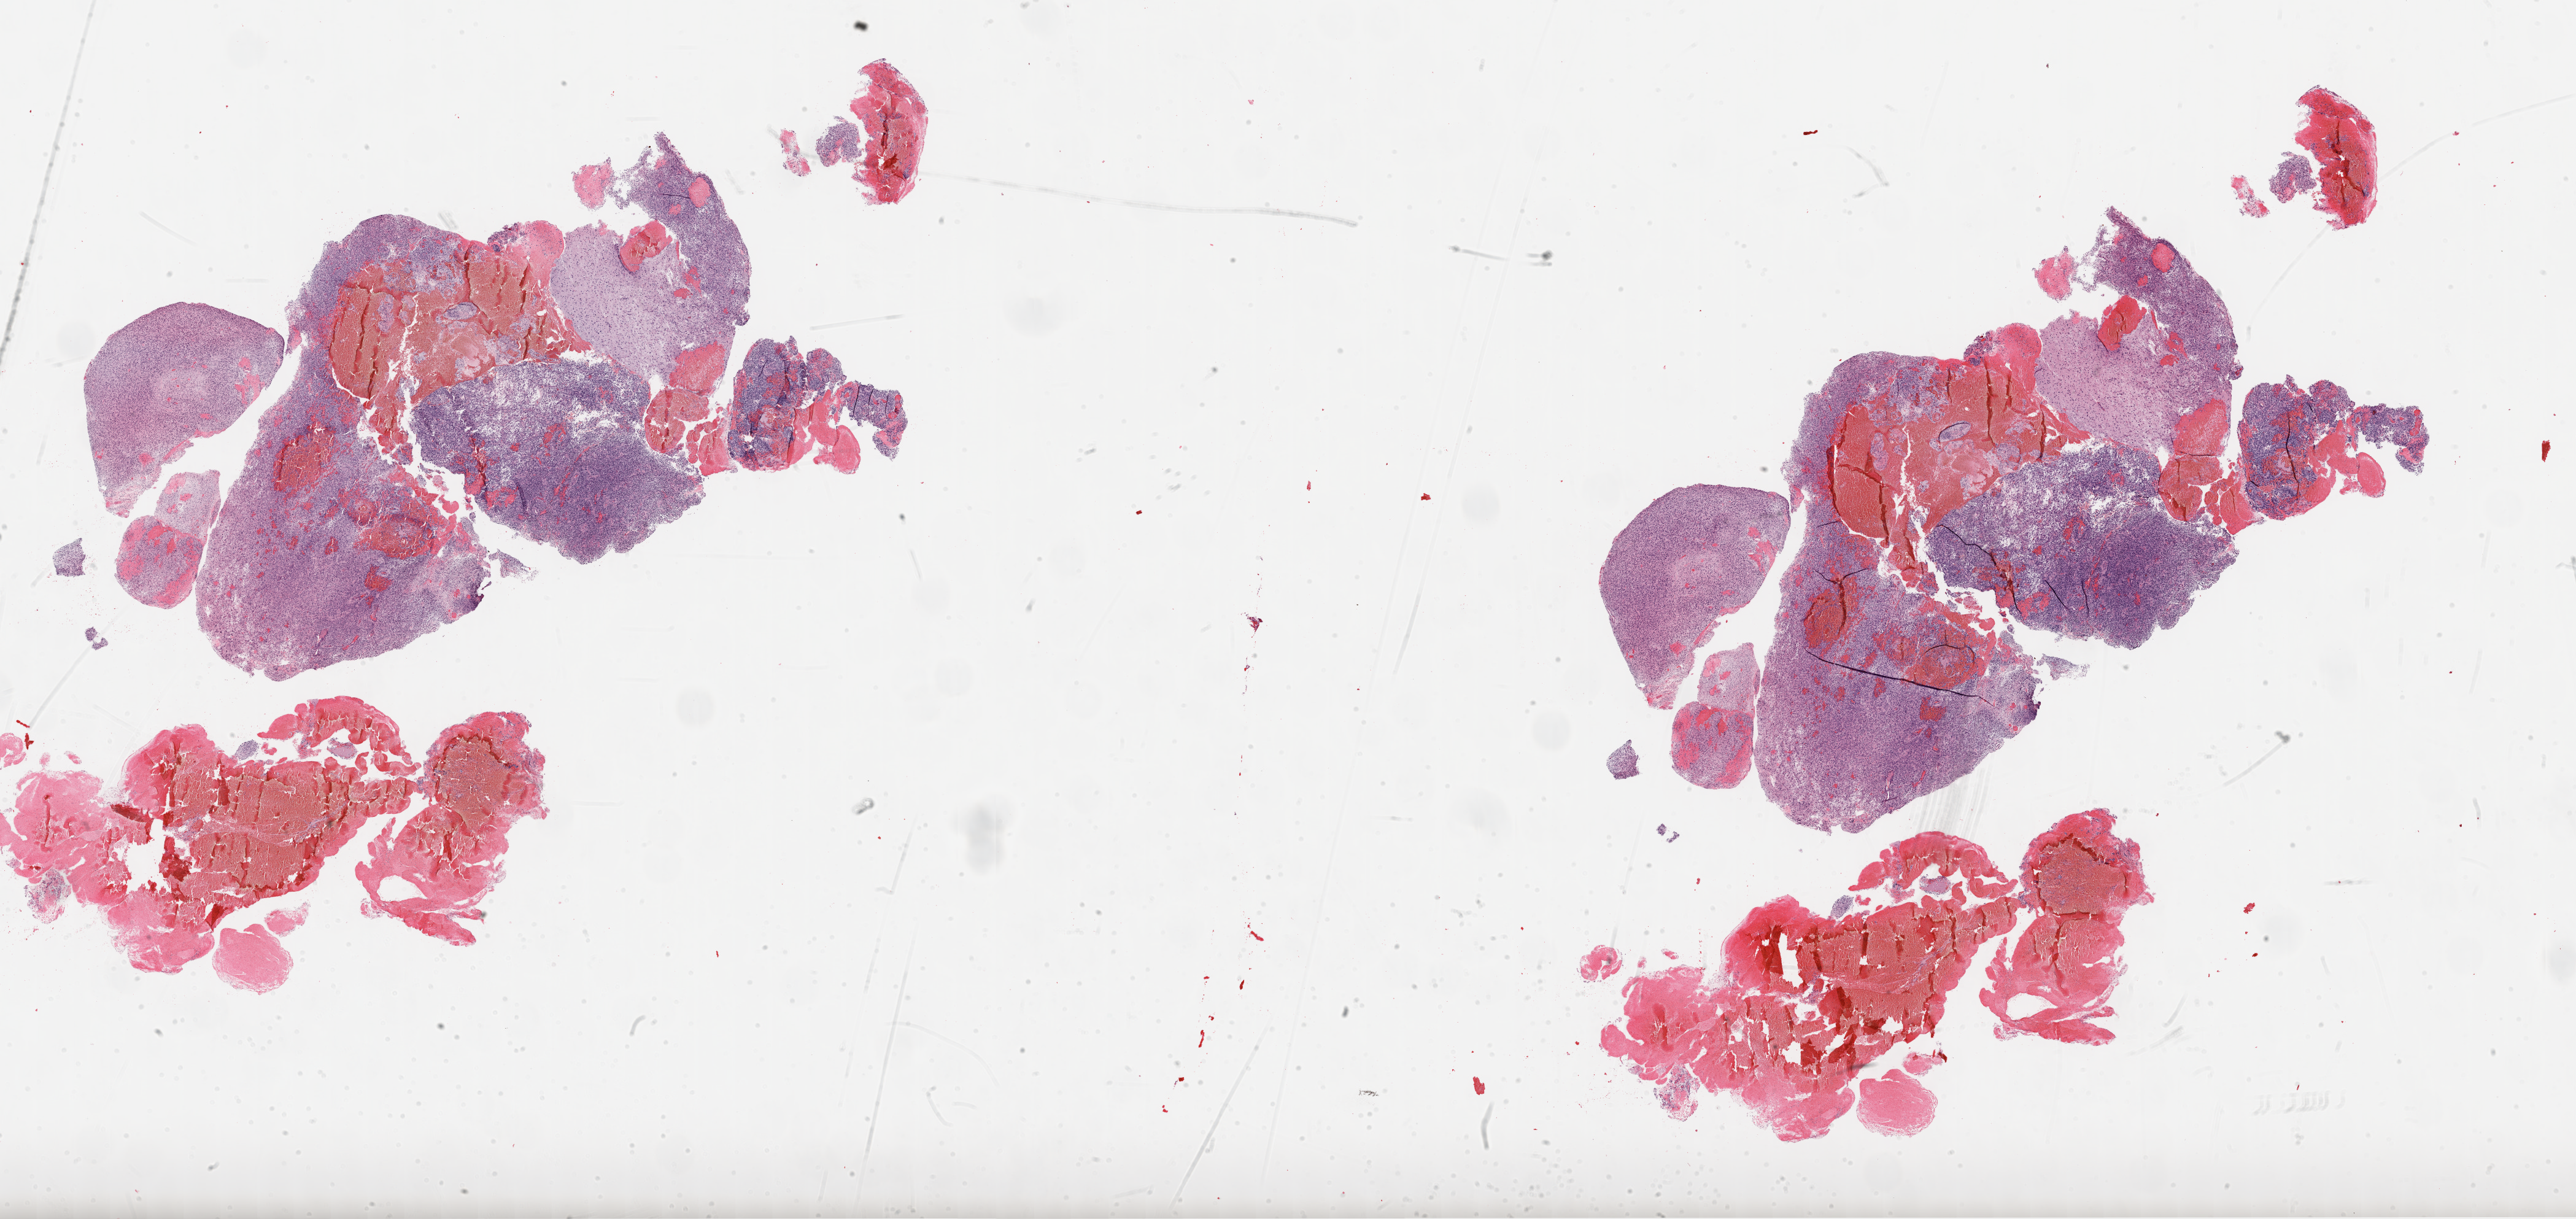
Digitized Hematoxylin and eosin (H&E) stained tissue section (whole slide) — whole scanned area (about 33.8 x 16.0 mm) shown as a low-resolution overview. Formalin-fixed paraffin-embedded (FFPE) diagnostic section. Primary tumour sample from the brain. Male patient; age at initial diagnosis 54 years.
Pathologic diagnosis: Glioblastoma.